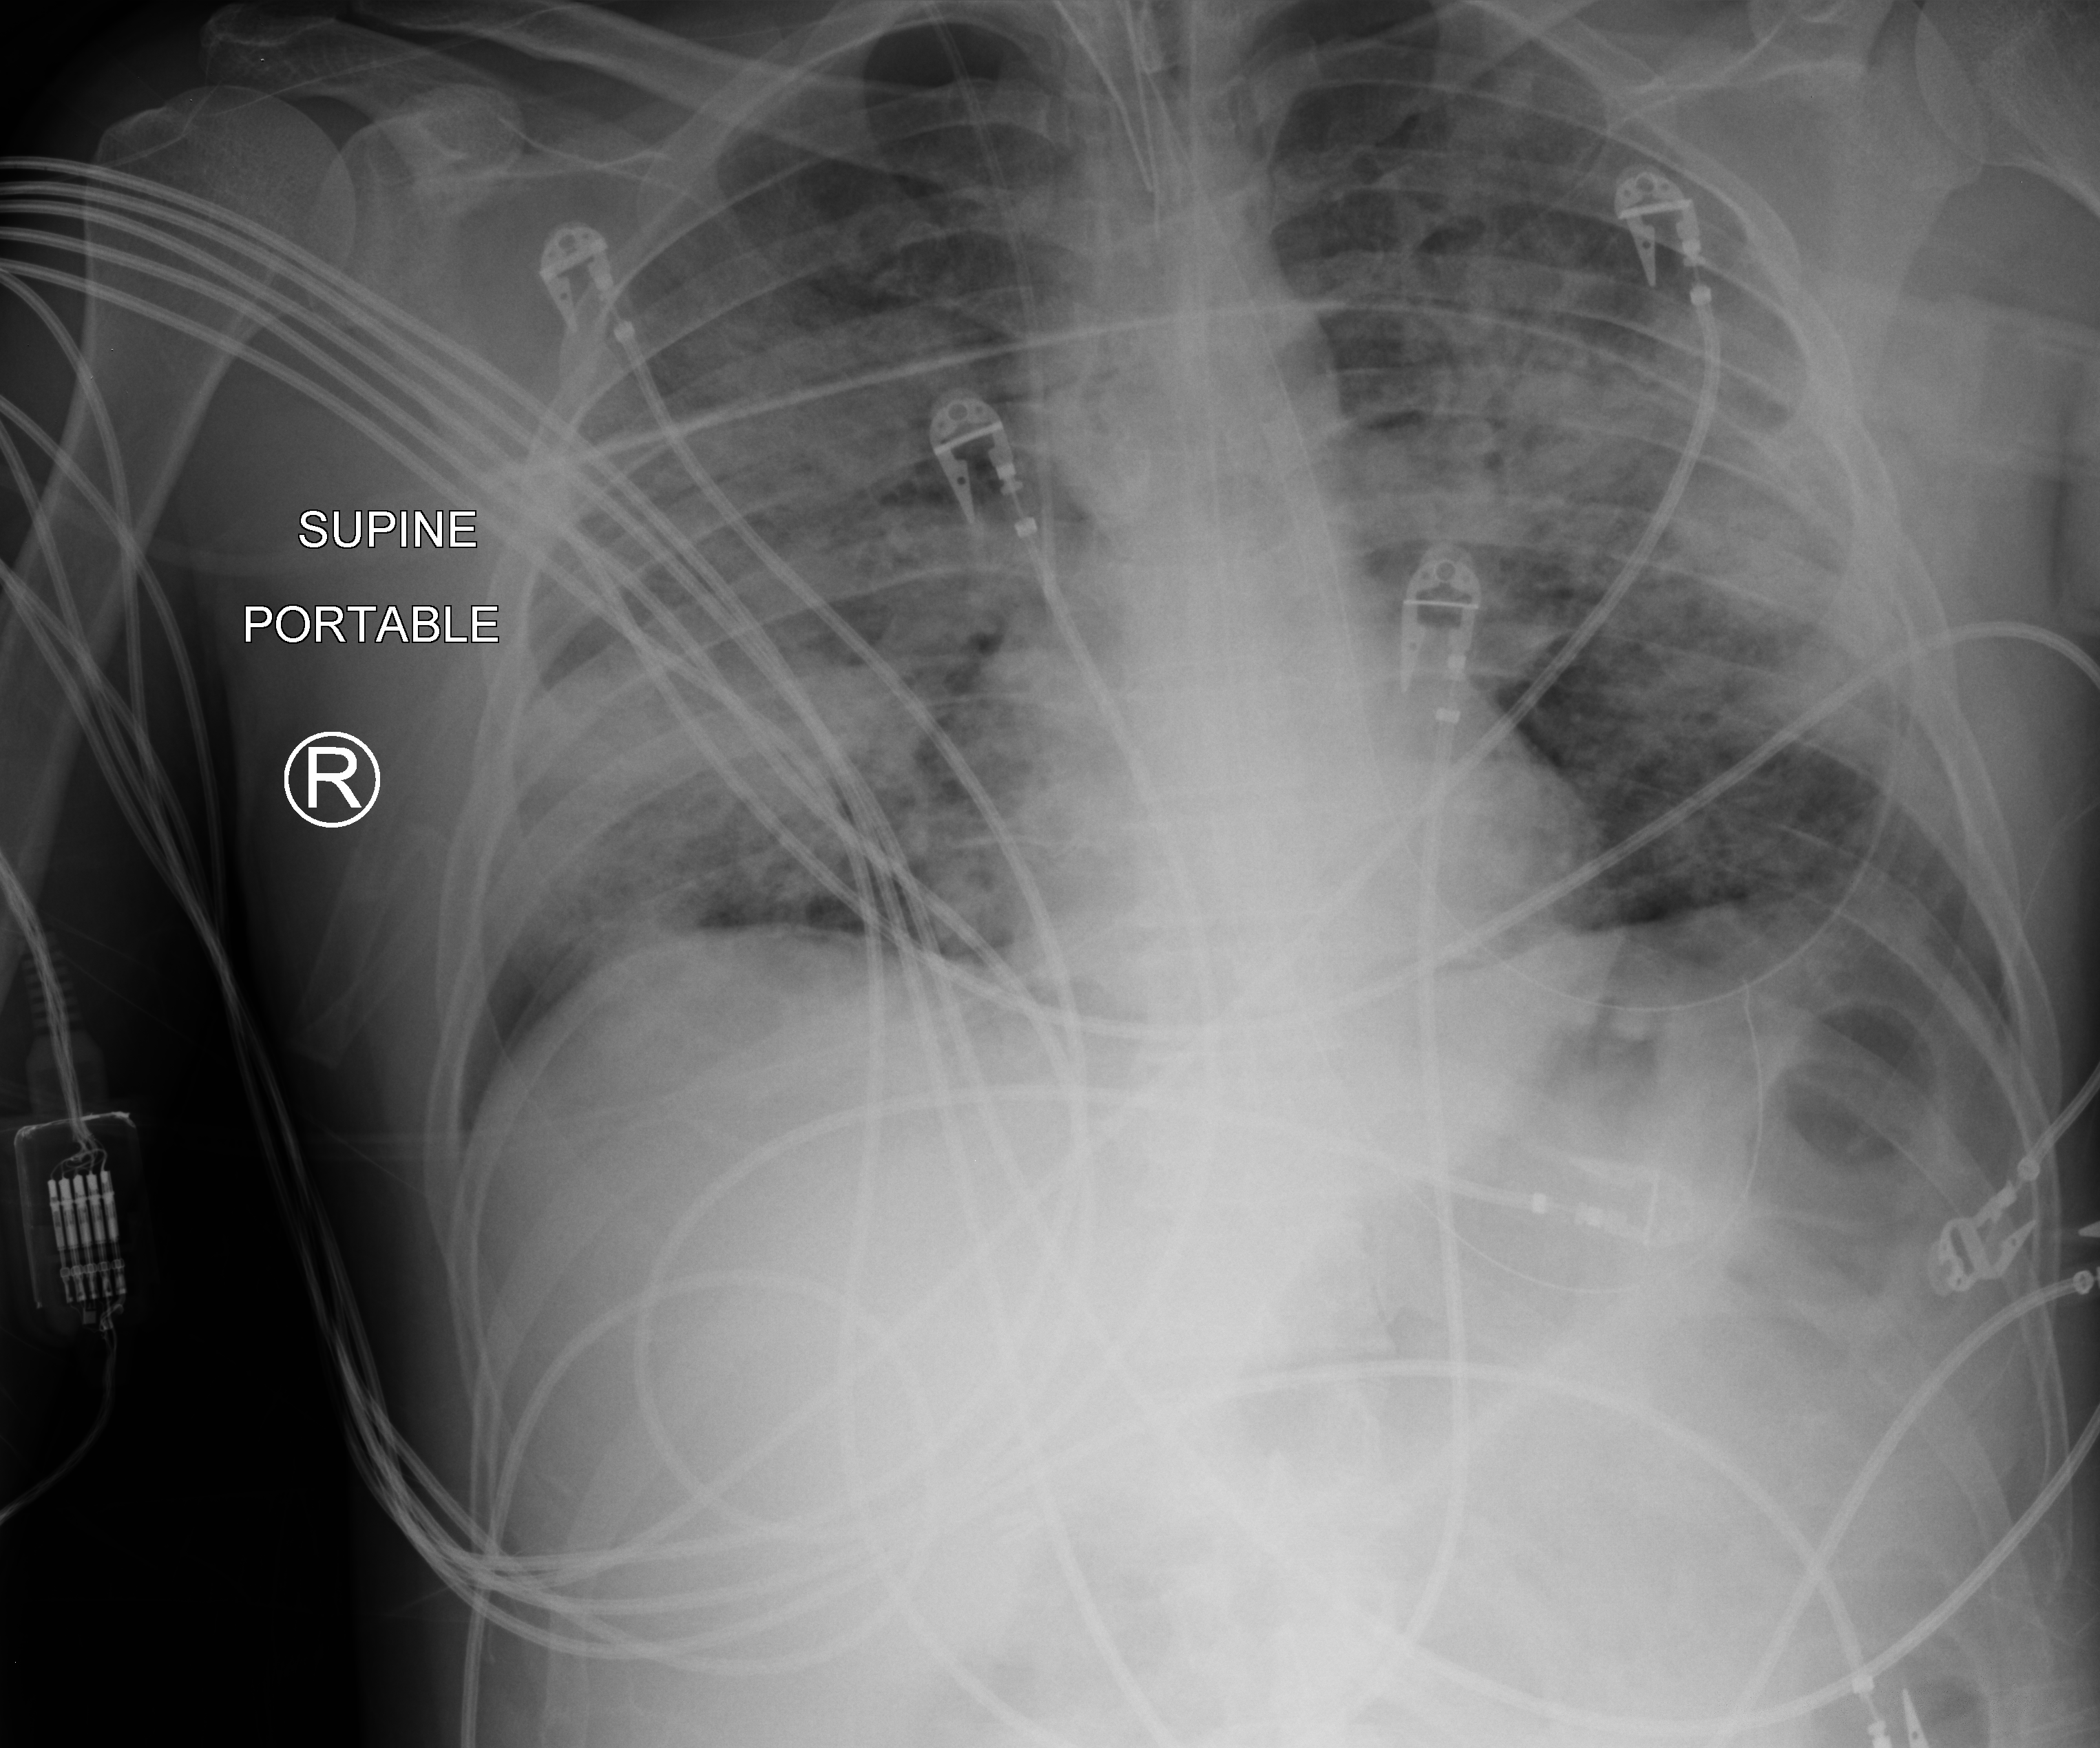
Portable chest radiograph; anteroposterior (AP) projection. Male patient hospitalised with COVID-19, age 18–59 years.
Admission-level facts for this patient (not findings on this image; timing relative to this image not recorded):
- mechanically ventilated during this hospital stay: yes
- chronic kidney disease (admission record): no